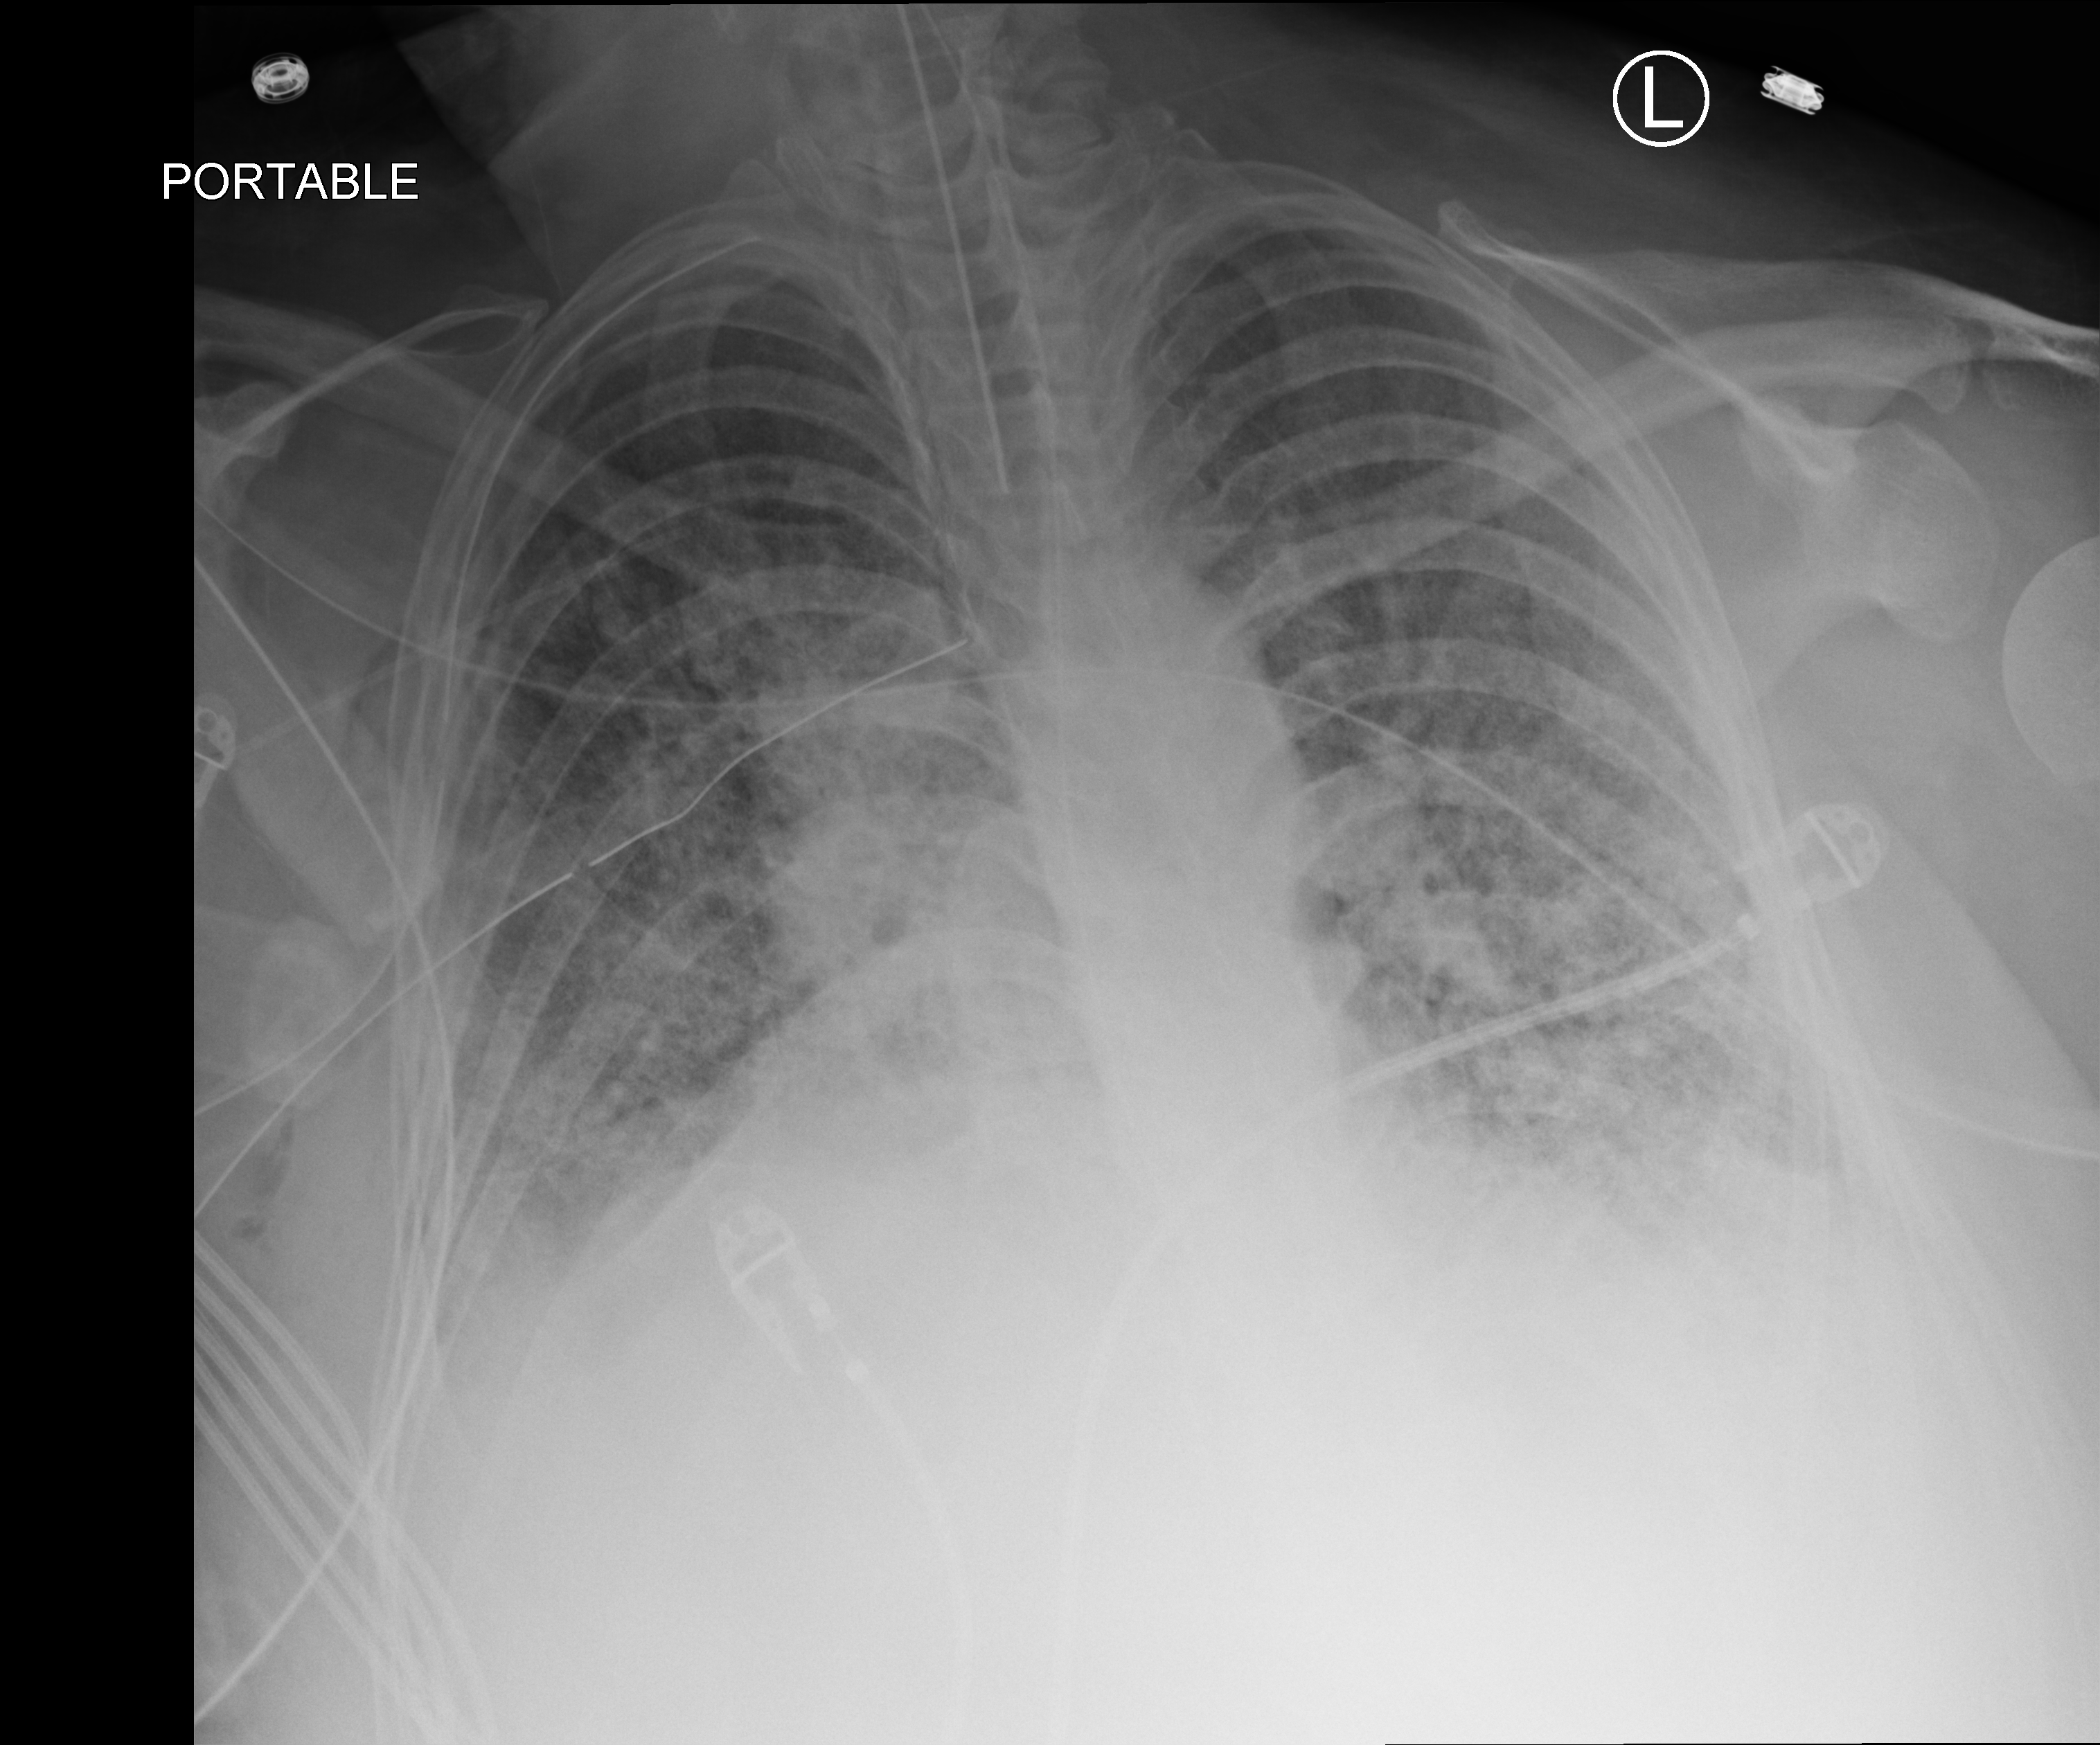
Portable chest radiograph; anteroposterior (AP) projection. Adult patient hospitalised with COVID-19, age 18–59 years.
Hospital-stay facts (about this admission, not read from this image; timing relative to this image not recorded): admitted to intensive care during this hospital stay: yes; chronic kidney disease (admission record): no.